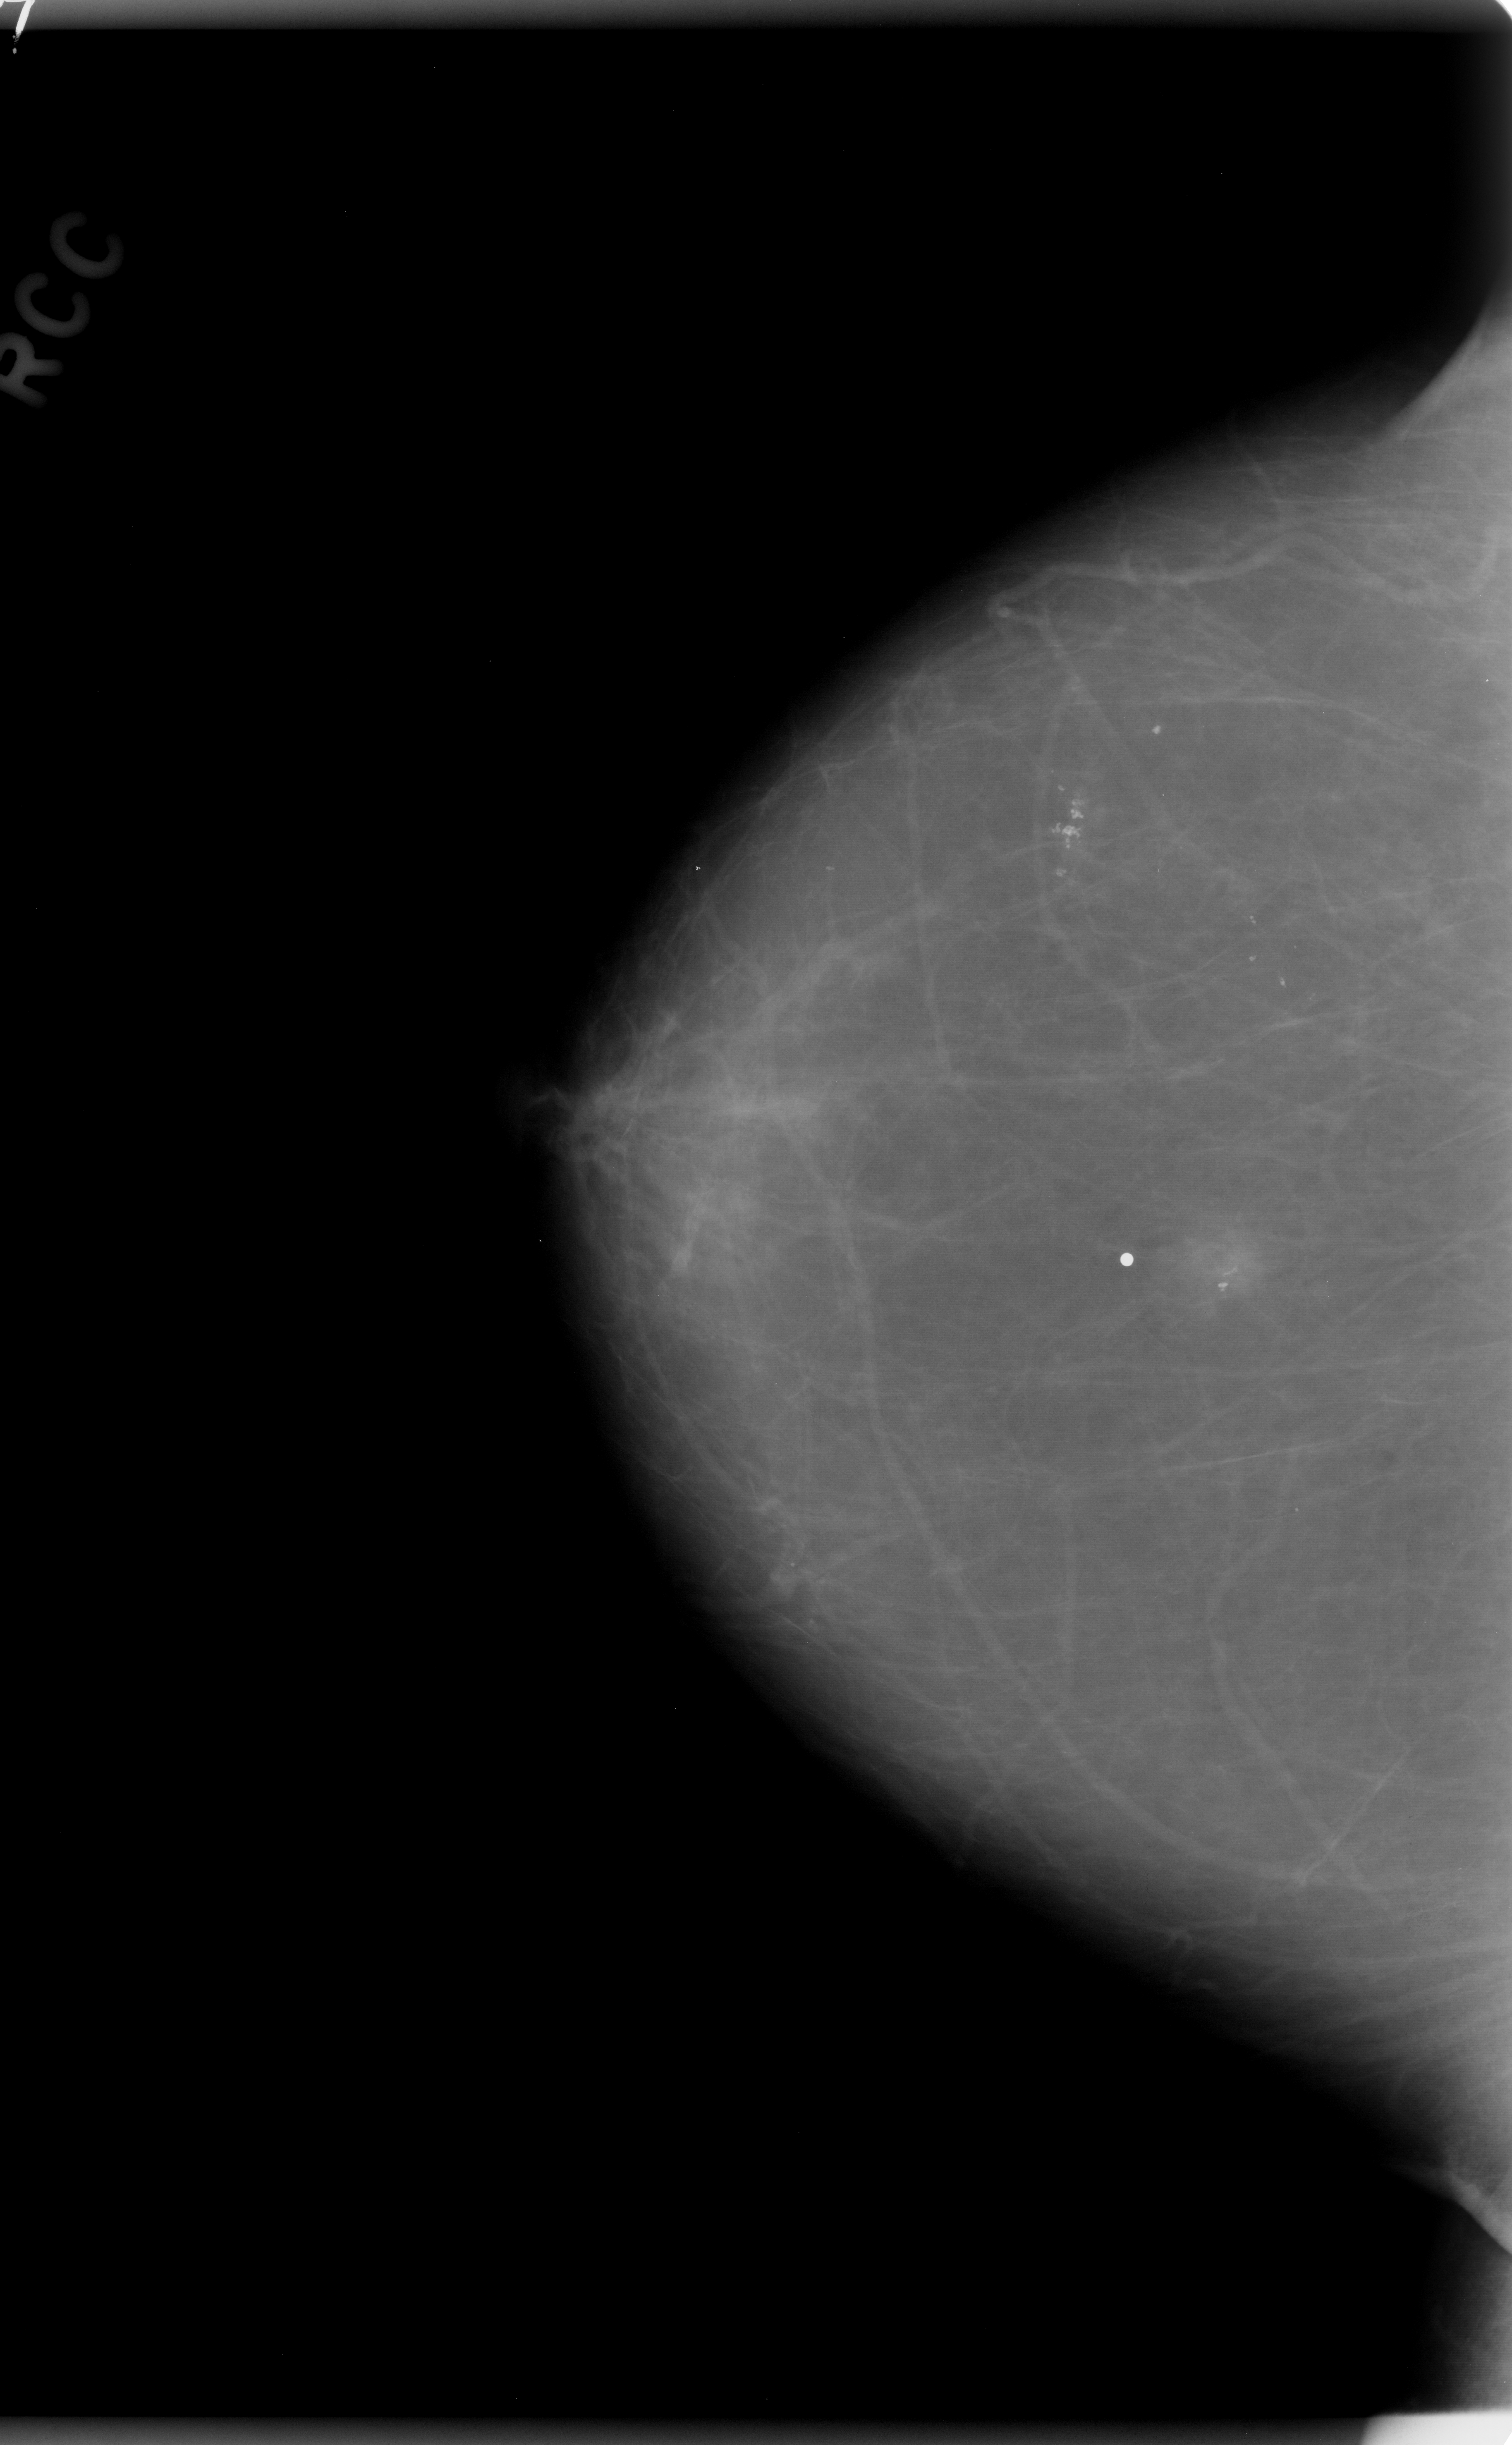
Digitized screen-film mammogram, right breast, CC view, BI-RADS breast density category 1 (scale 1–4).
Abnormality record for this image: Finding 1 of 3: calcifications, morphology pleomorphic, distribution clustered; BI-RADS assessment category 4; subtlety rating 5 on a 1 (subtle) to 5 (obvious) scale; pathology result (as recorded, not read from the image): benign. Finding 2 of 3: calcifications, morphology punctate, distribution clustered; BI-RADS assessment category 4; subtlety rating 5 on a 1 (subtle) to 5 (obvious) scale; pathology (as recorded): benign. Finding 3 of 3: calcifications, morphology fine linear branching, distribution clustered; BI-RADS assessment category 4; pathology result (as recorded, not read from the image): benign.